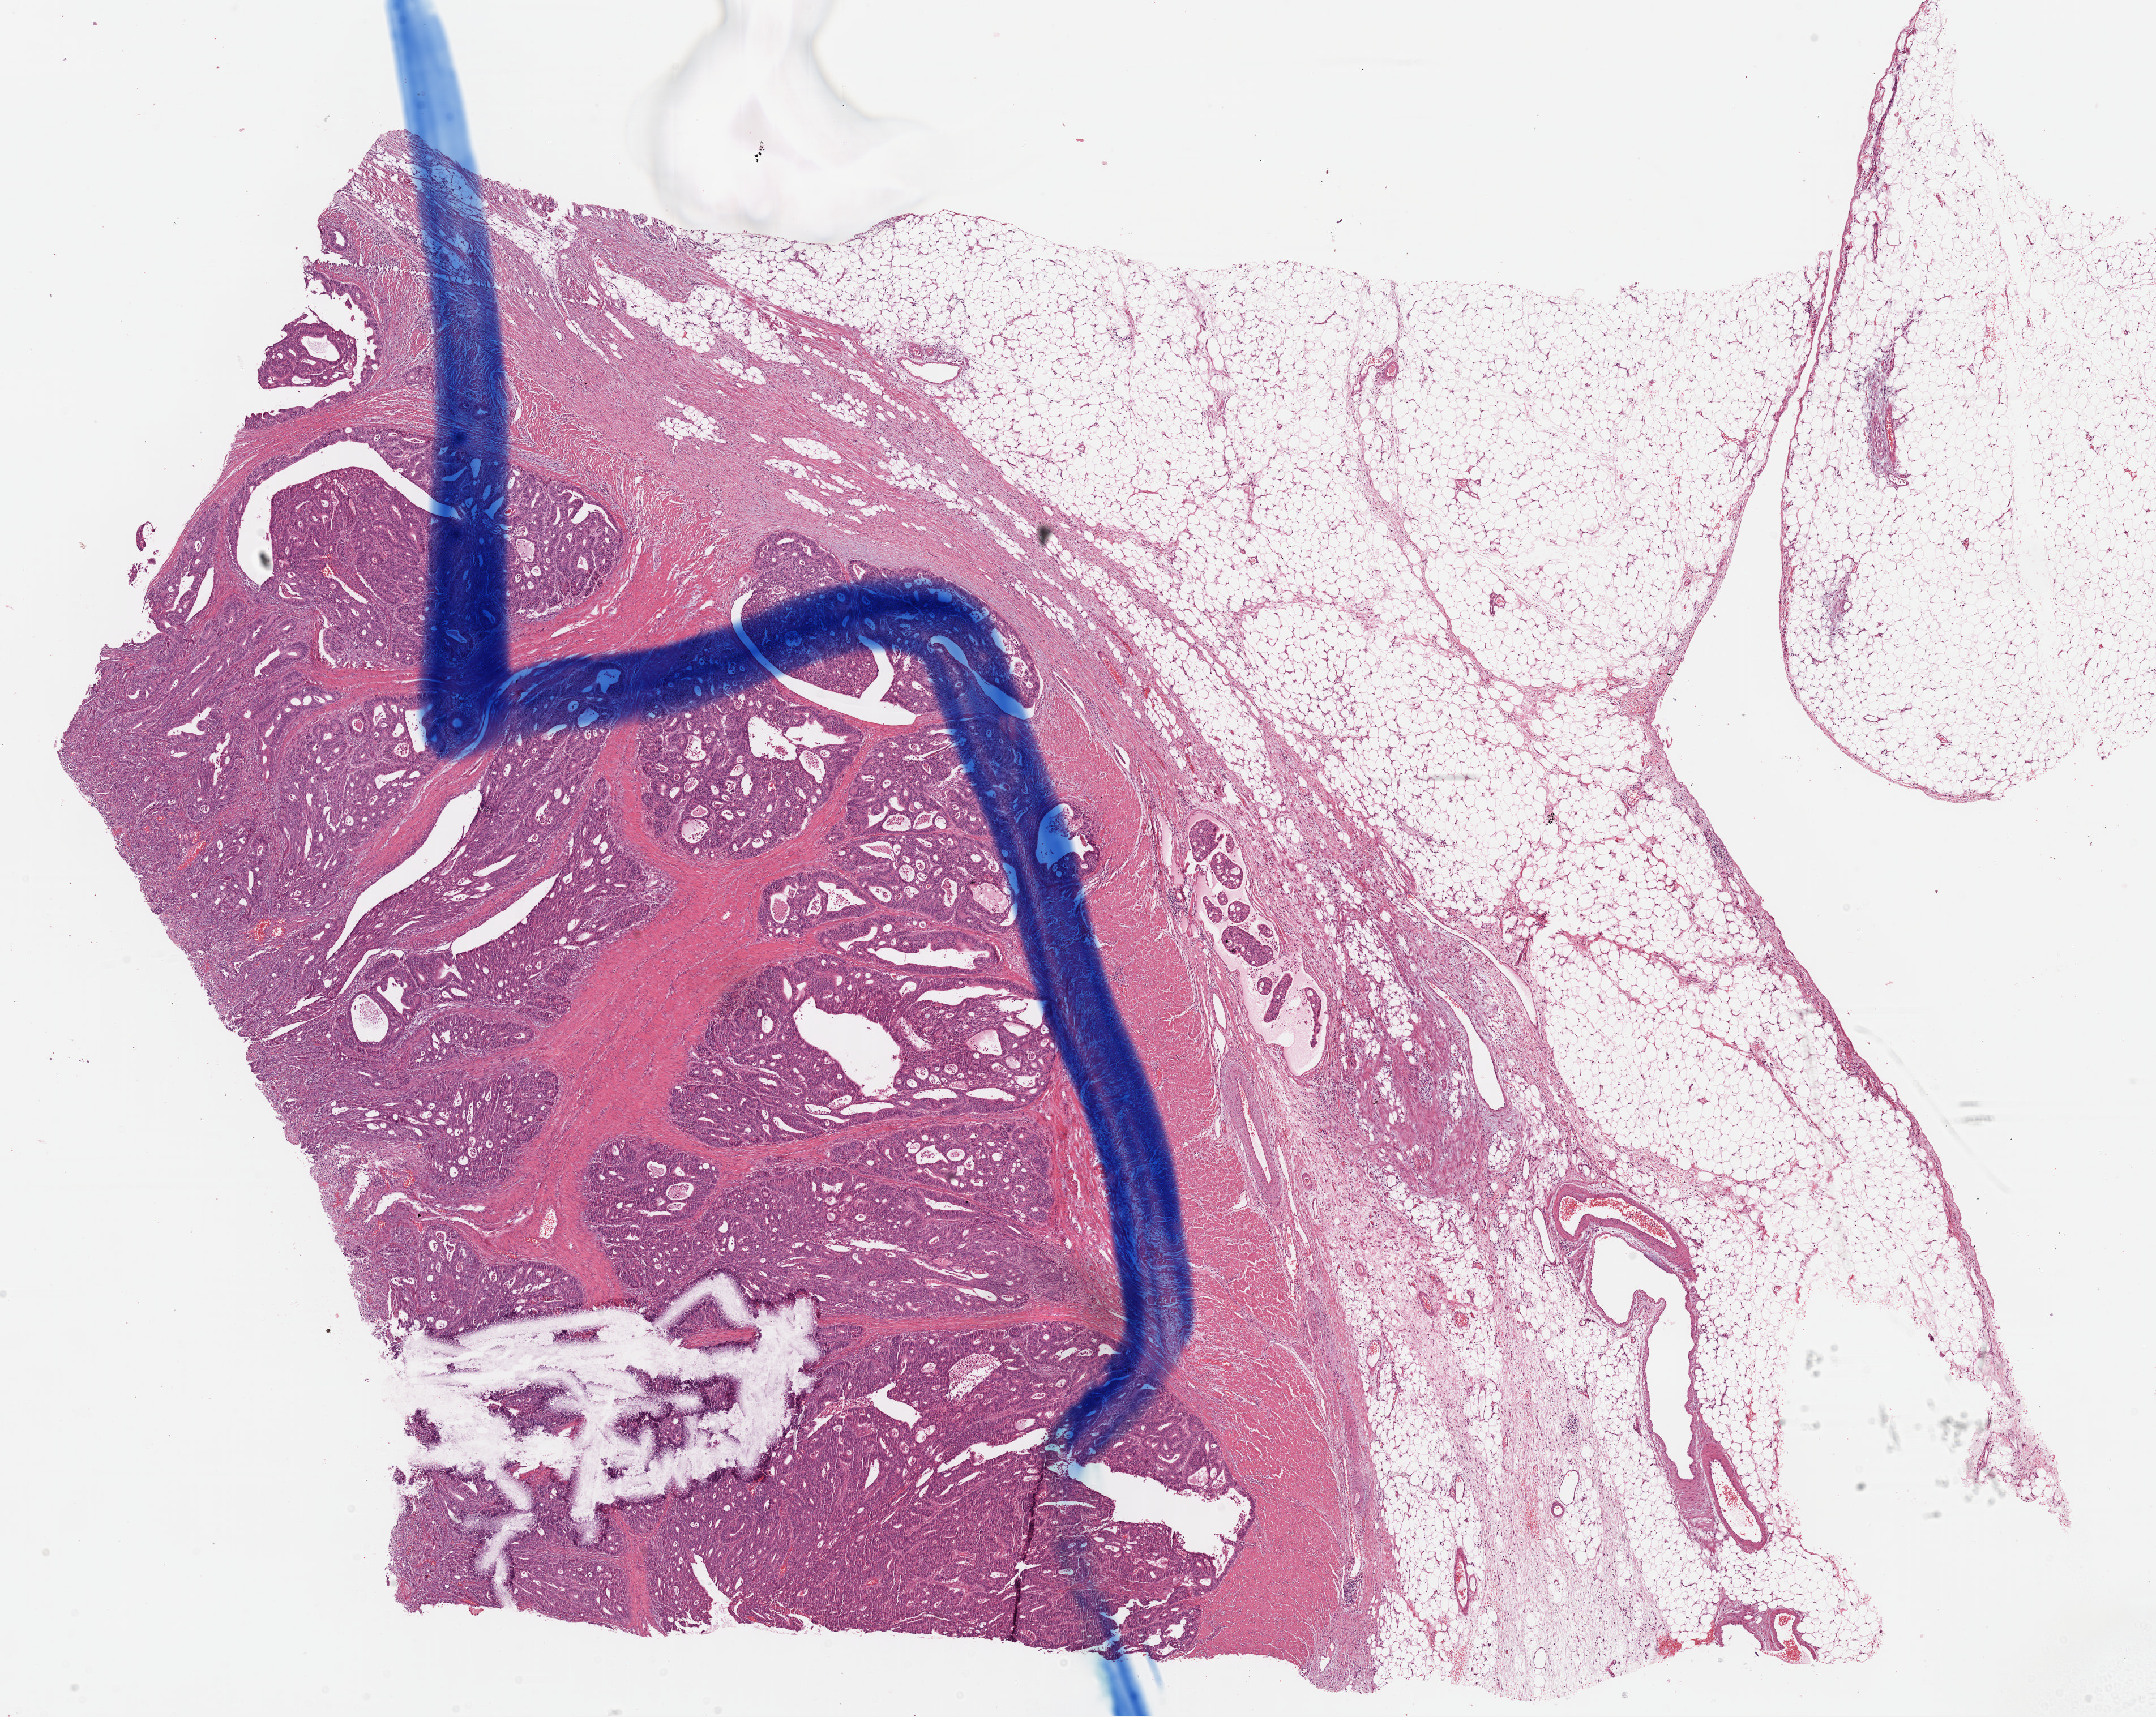
Whole-slide histology image, H&E — low-resolution overview of the scanned area, about 15.0 x 12.0 mm (slide scanned at 40x). FFPE section. Primary tumour sample from the colon. Female, age 50 years at initial diagnosis.
Diagnosis: Adenocarcinoma, NOS (ascending colon).